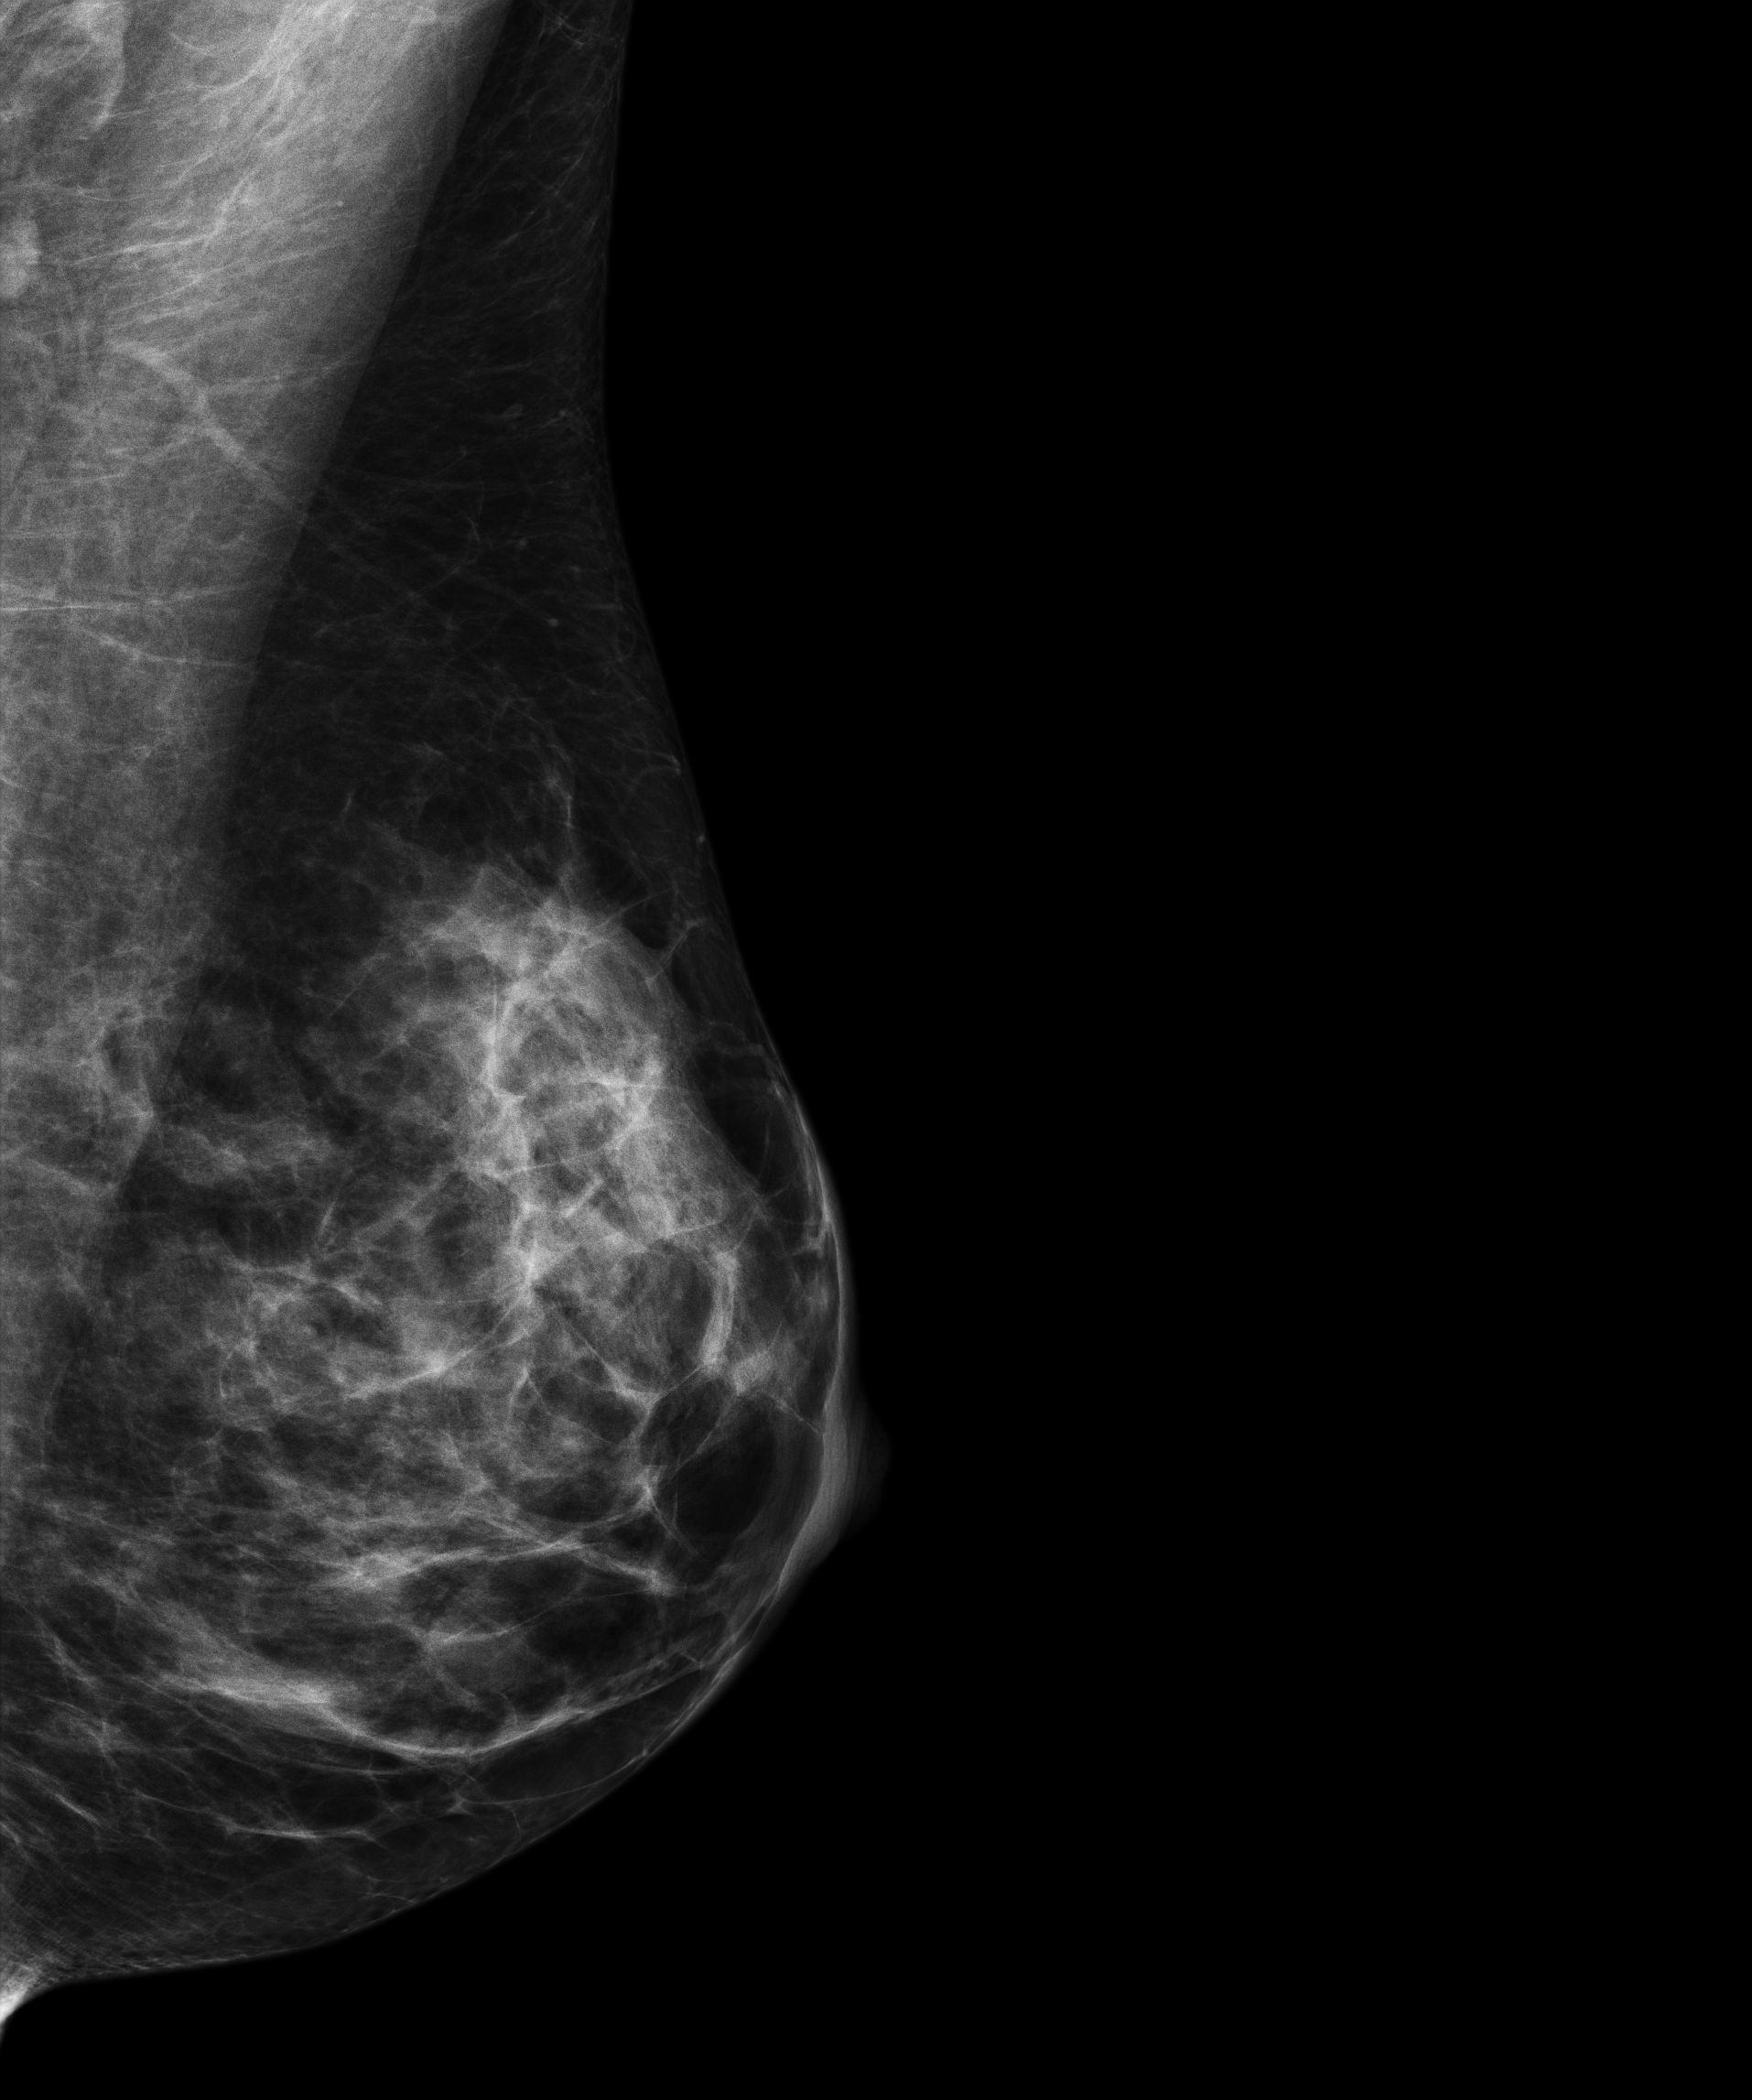
Digital mammogram (FFDM); left breast; MLO view; annual screening mammography examination. Patient aged 45 years (female).
Final BI-RADS category for the screening round (tomosynthesis exam, both breasts): category 1.